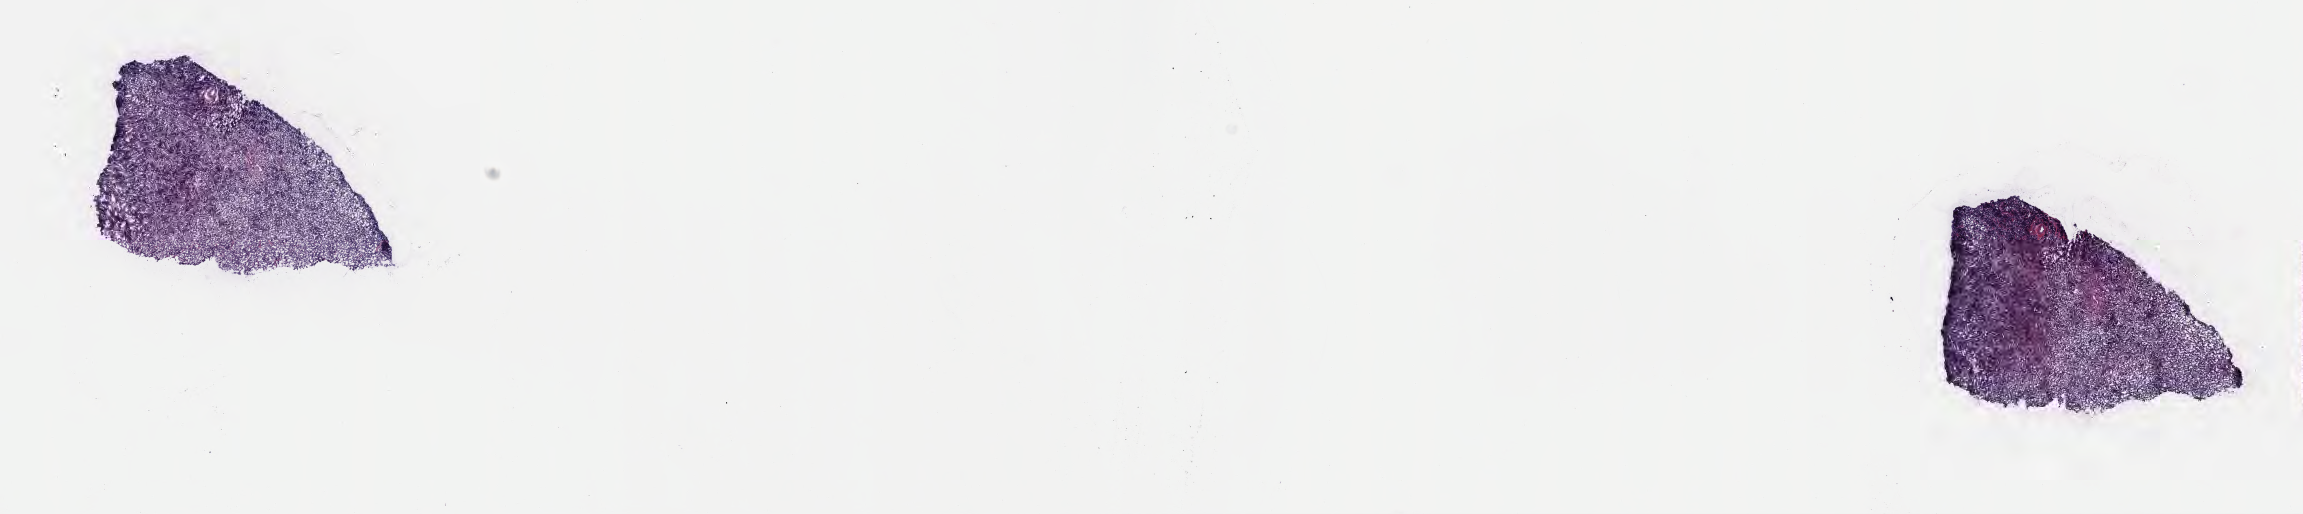
Digitized hematoxylin and eosin (H&E)-stained section — shown as a low-resolution overview of the whole scanned area (about 18.6 x 4.2 mm). Frozen section (tissue freezing medium). Specimen: primary tumor. Site: mandible. Patient male; aged 19. Slide review estimates, as recorded: tumor cells 85%, tumor nuclei 90%, stromal cells 10%, necrosis 5%, normal cells 0%. Inflammatory infiltration, as recorded: lymphocyte infiltration 70%, monocyte infiltration 15%, neutrophil infiltration 5%.
* Ann Arbor stage (patient): Stage III
* diagnosis: Burkitt lymphoma, NOS
* section: bottom of the tissue portion